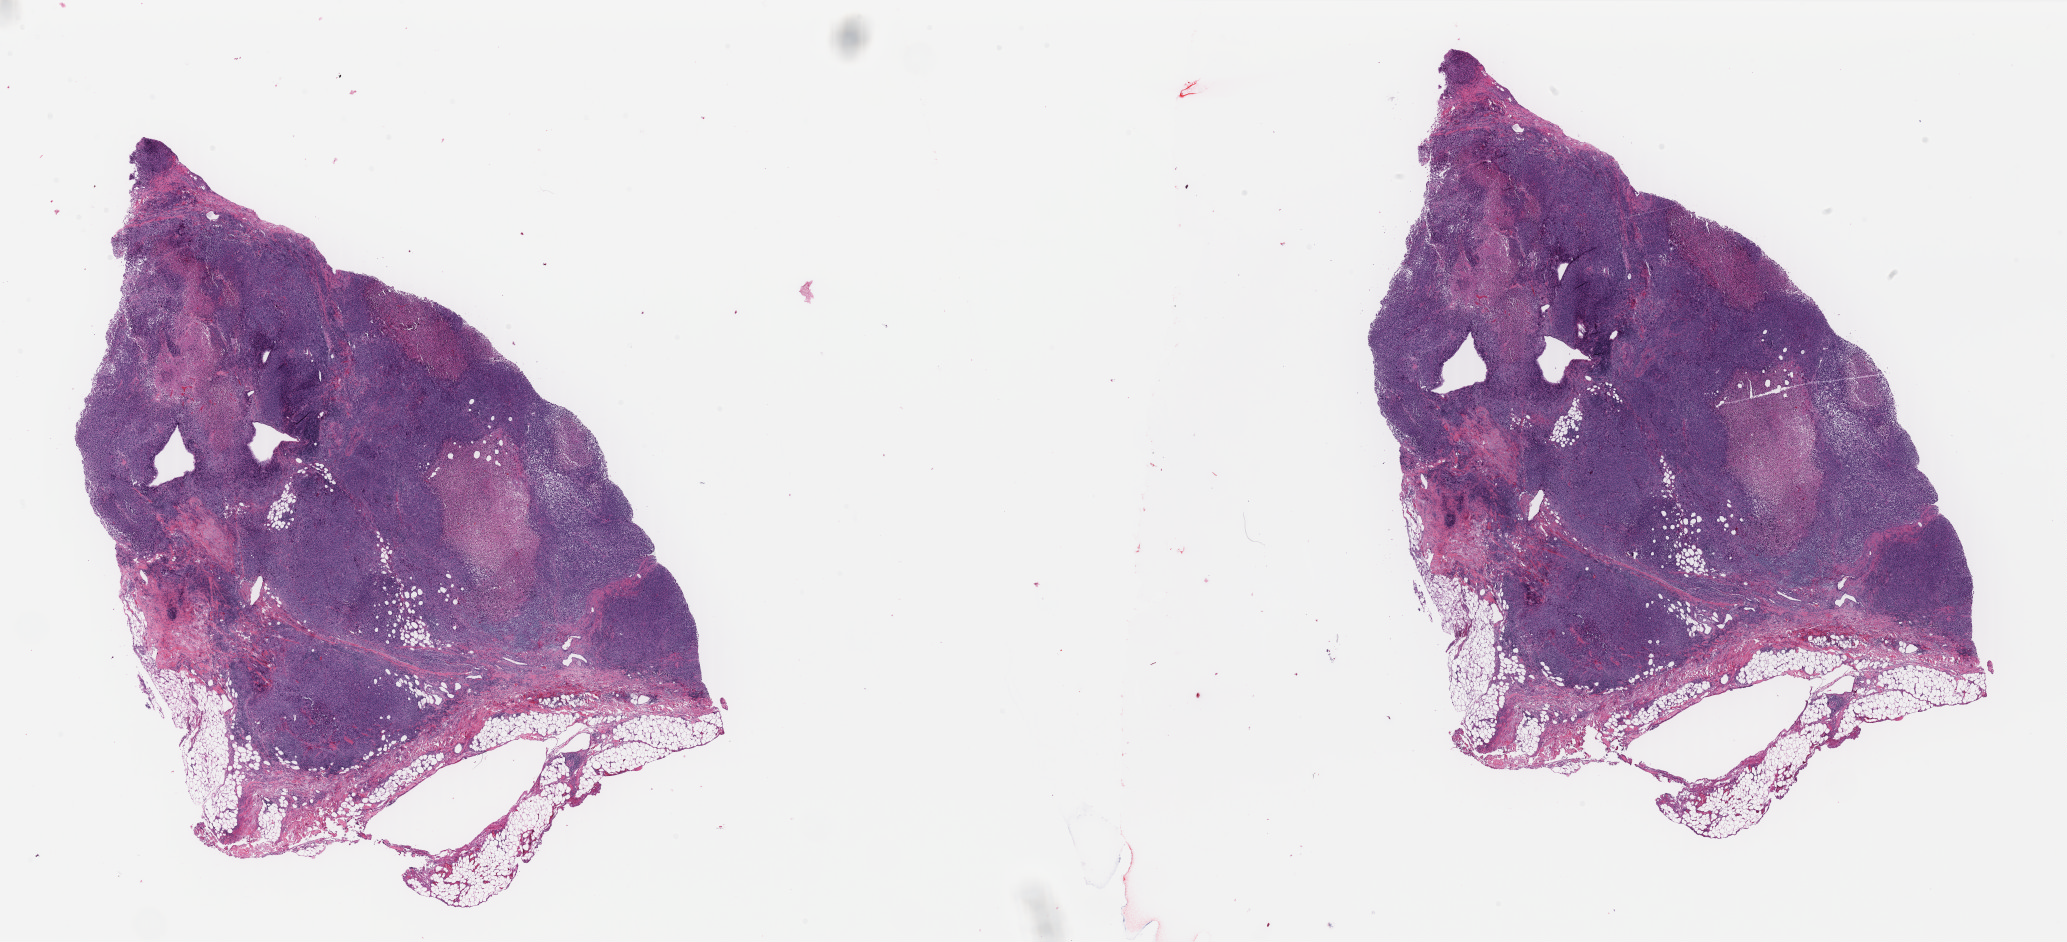
Digitized H&E tissue section (whole slide) — low-resolution overview of the scanned area, about 32.7 x 14.9 mm (slide scanned at 40x). FFPE section. Sample: primary tumour, skin. Female patient; age at initial diagnosis 63 years.
Diagnosis: Malignant melanoma, NOS.